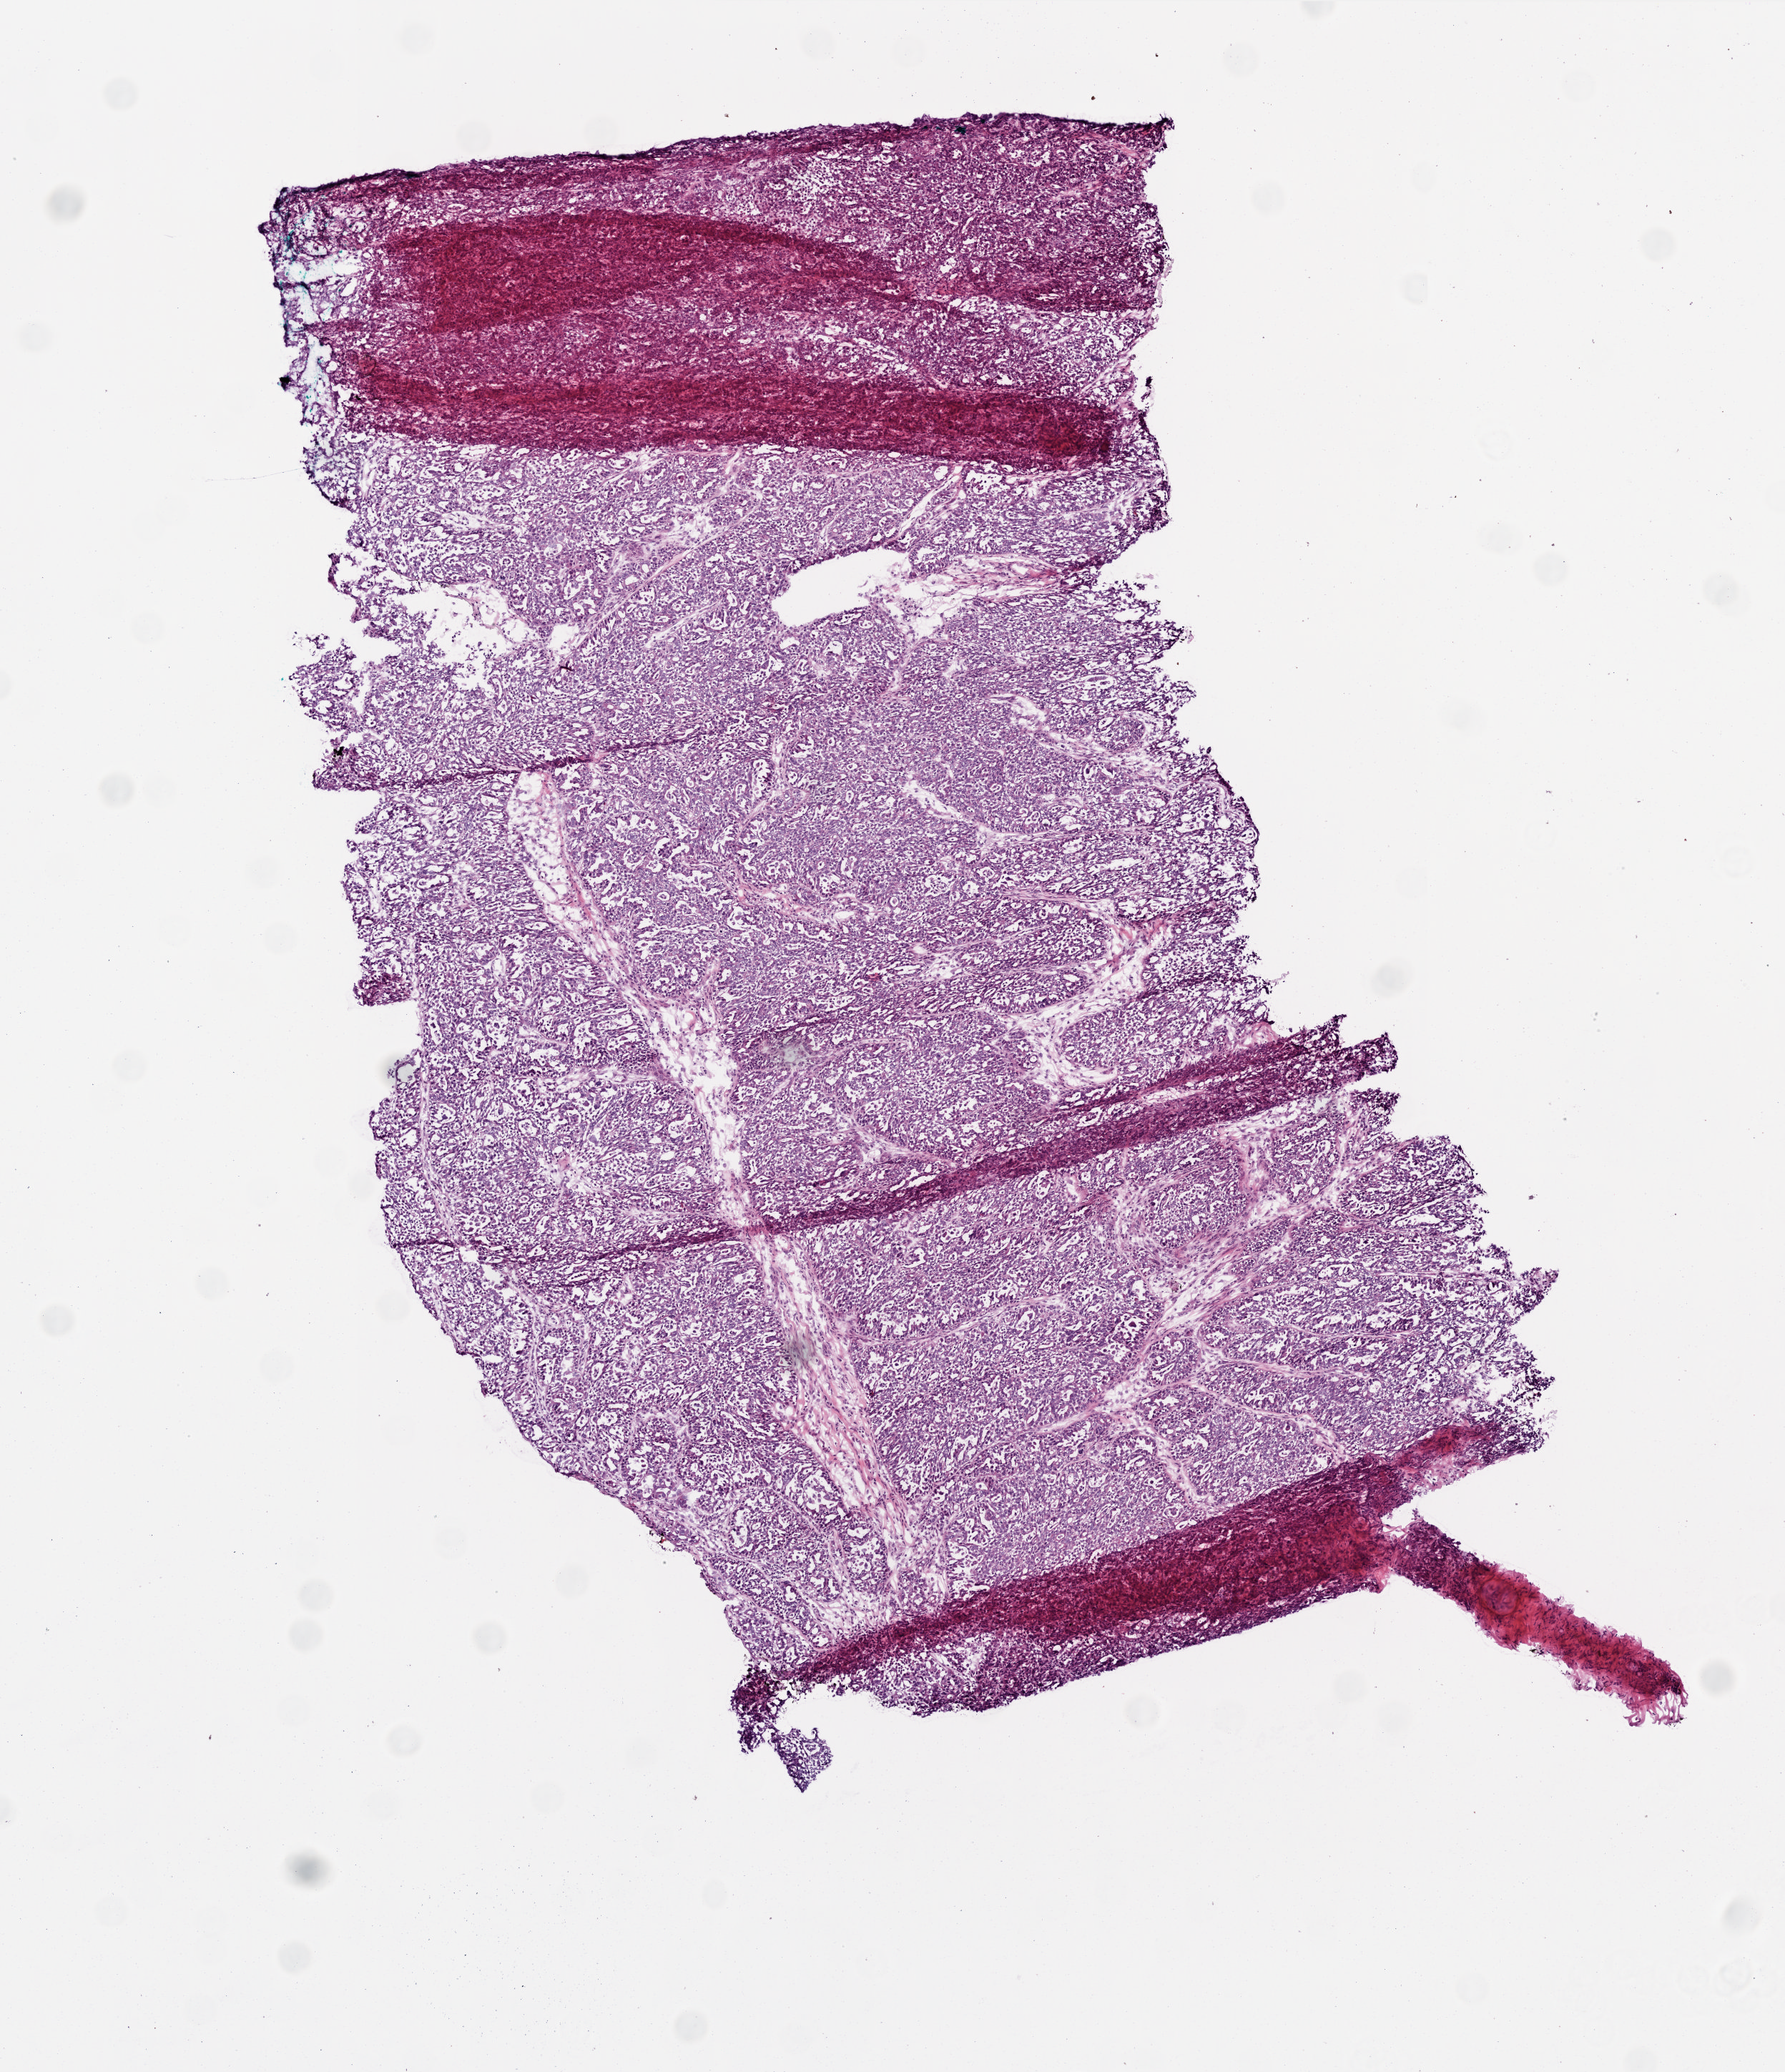
Whole-slide histology image, H&E-stained — a low-resolution overview of the entire scanned area, about 5.0 x 5.8 mm. Frozen section from the bottom of the tissue portion. Primary tumour sample from the ovary. Female patient; age at initial diagnosis 55 years. Composition of this section per pathologist review: tumour cells 95%, tumour nuclei 98%.
Pathologic diagnosis: Serous cystadenocarcinoma, NOS.